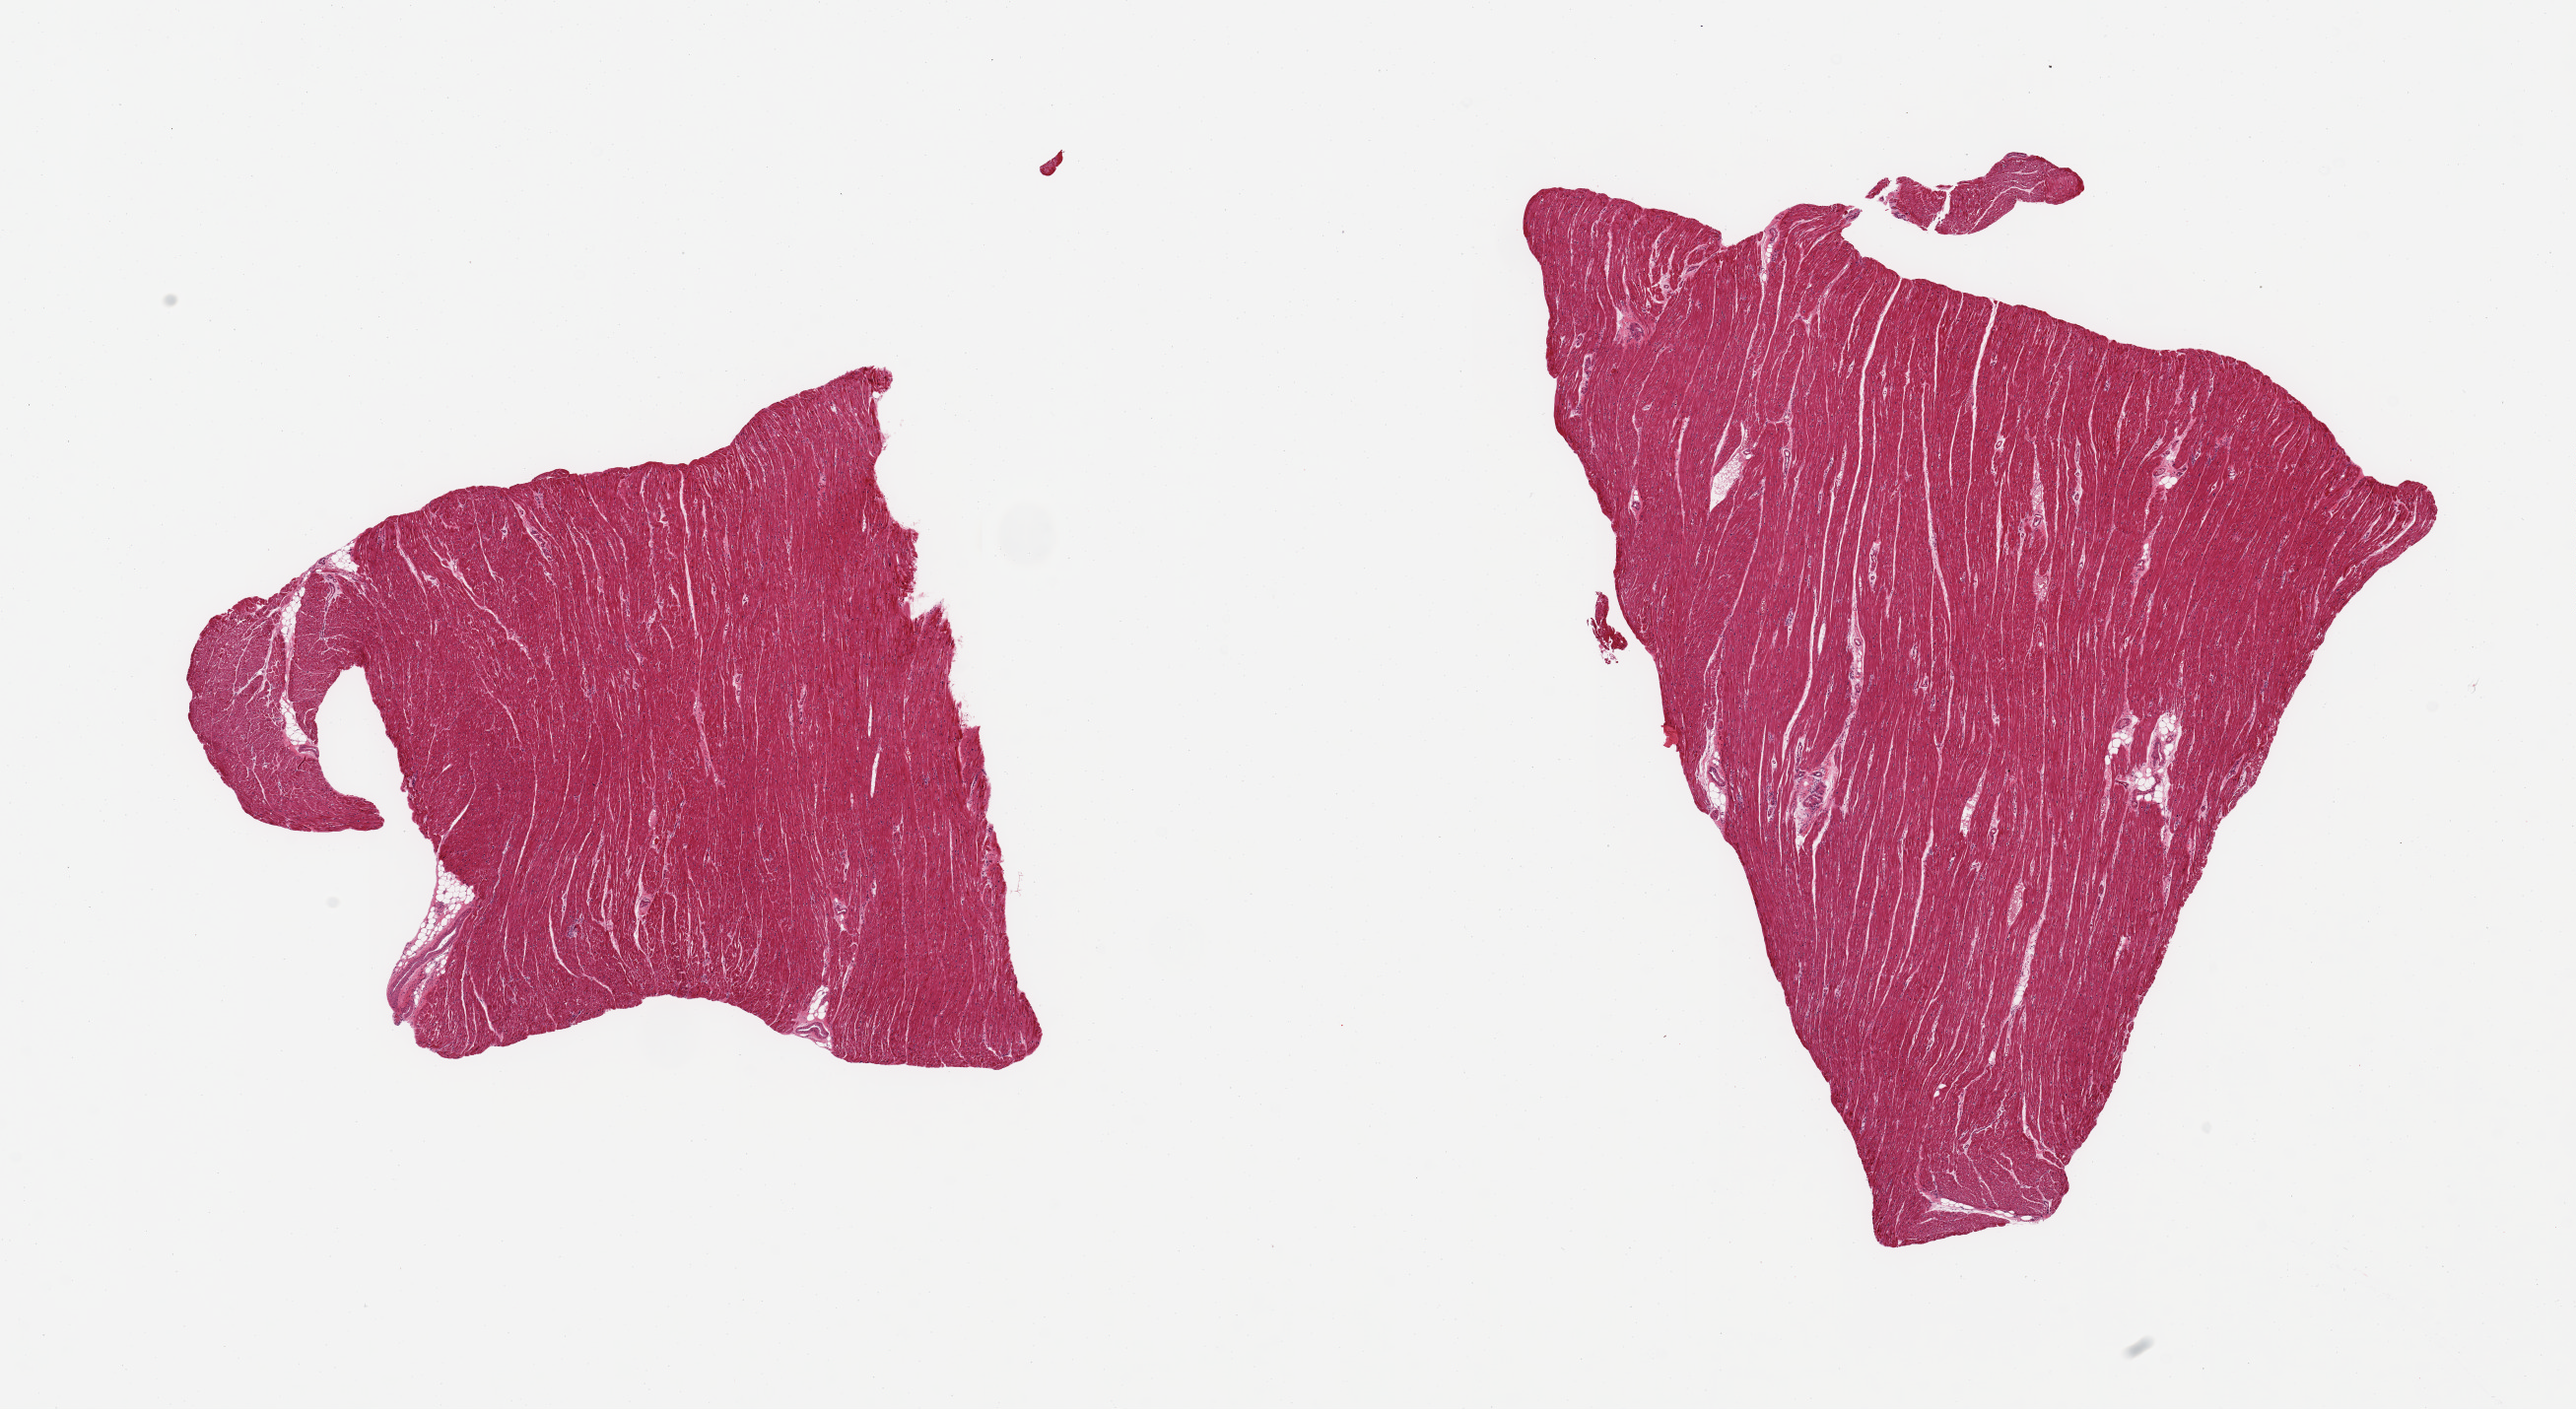
Whole-slide image, H&E stain — a low-resolution overview of the entire scanned area, about 20.7 x 11.3 mm (acquisition: 20x scan); PAXgene-fixed, paraffin-embedded tissue; target tissue: heart; donor tissue sample. Donor: male.
Review note (as recorded): 2 pieces; fatty tissue around the capillaries 5% content.